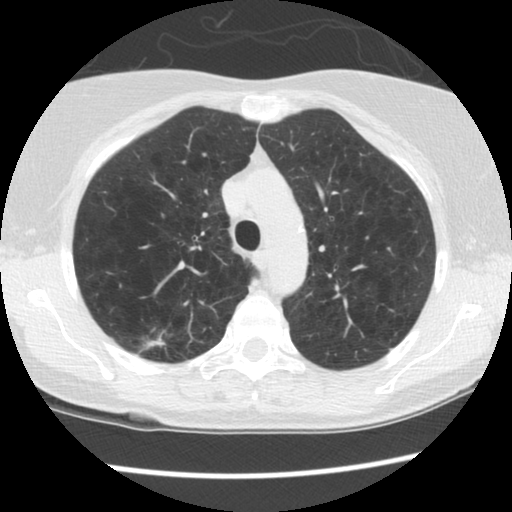
Low-dose screening chest CT, one axial slice. Position 102 of 134 along the scan axis. Reconstruction kernel STANDARD. Lung window (W 1500 / L -600 HU). 2.5 mm slice thickness. 512 × 512 image matrix, field of view 319 × 319 mm.
Annotated regions visible in this slice (outlined manually by an expert reader):
- lesion 1 (tumor, upper lobe of right lung): bounding box <137,335,166,355> (left, top, right, bottom; pixels)